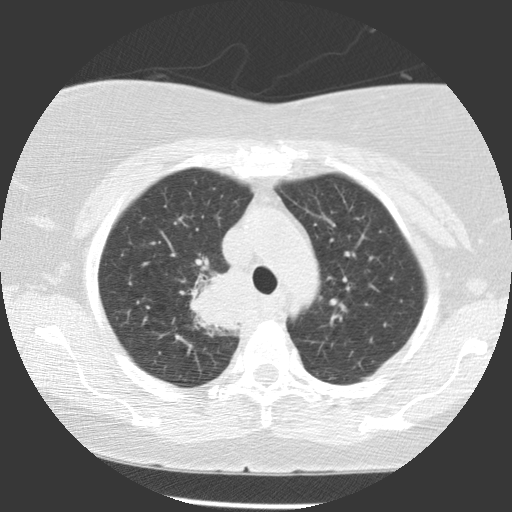
Low-dose screening chest CT, one axial slice. Slice 88 of 116 in the series (ordered by position). 140 kVp. Lung window (W 1500 / L -600 HU). 512 × 512 image matrix, field of view 320 × 320 mm.
Structures marked on this image (manually delineated by an expert):
- lesion 1 (tumor, upper lobe of right lung): bounding box (x1, y1, x2, y2) in pixels: (190, 265, 246, 335)